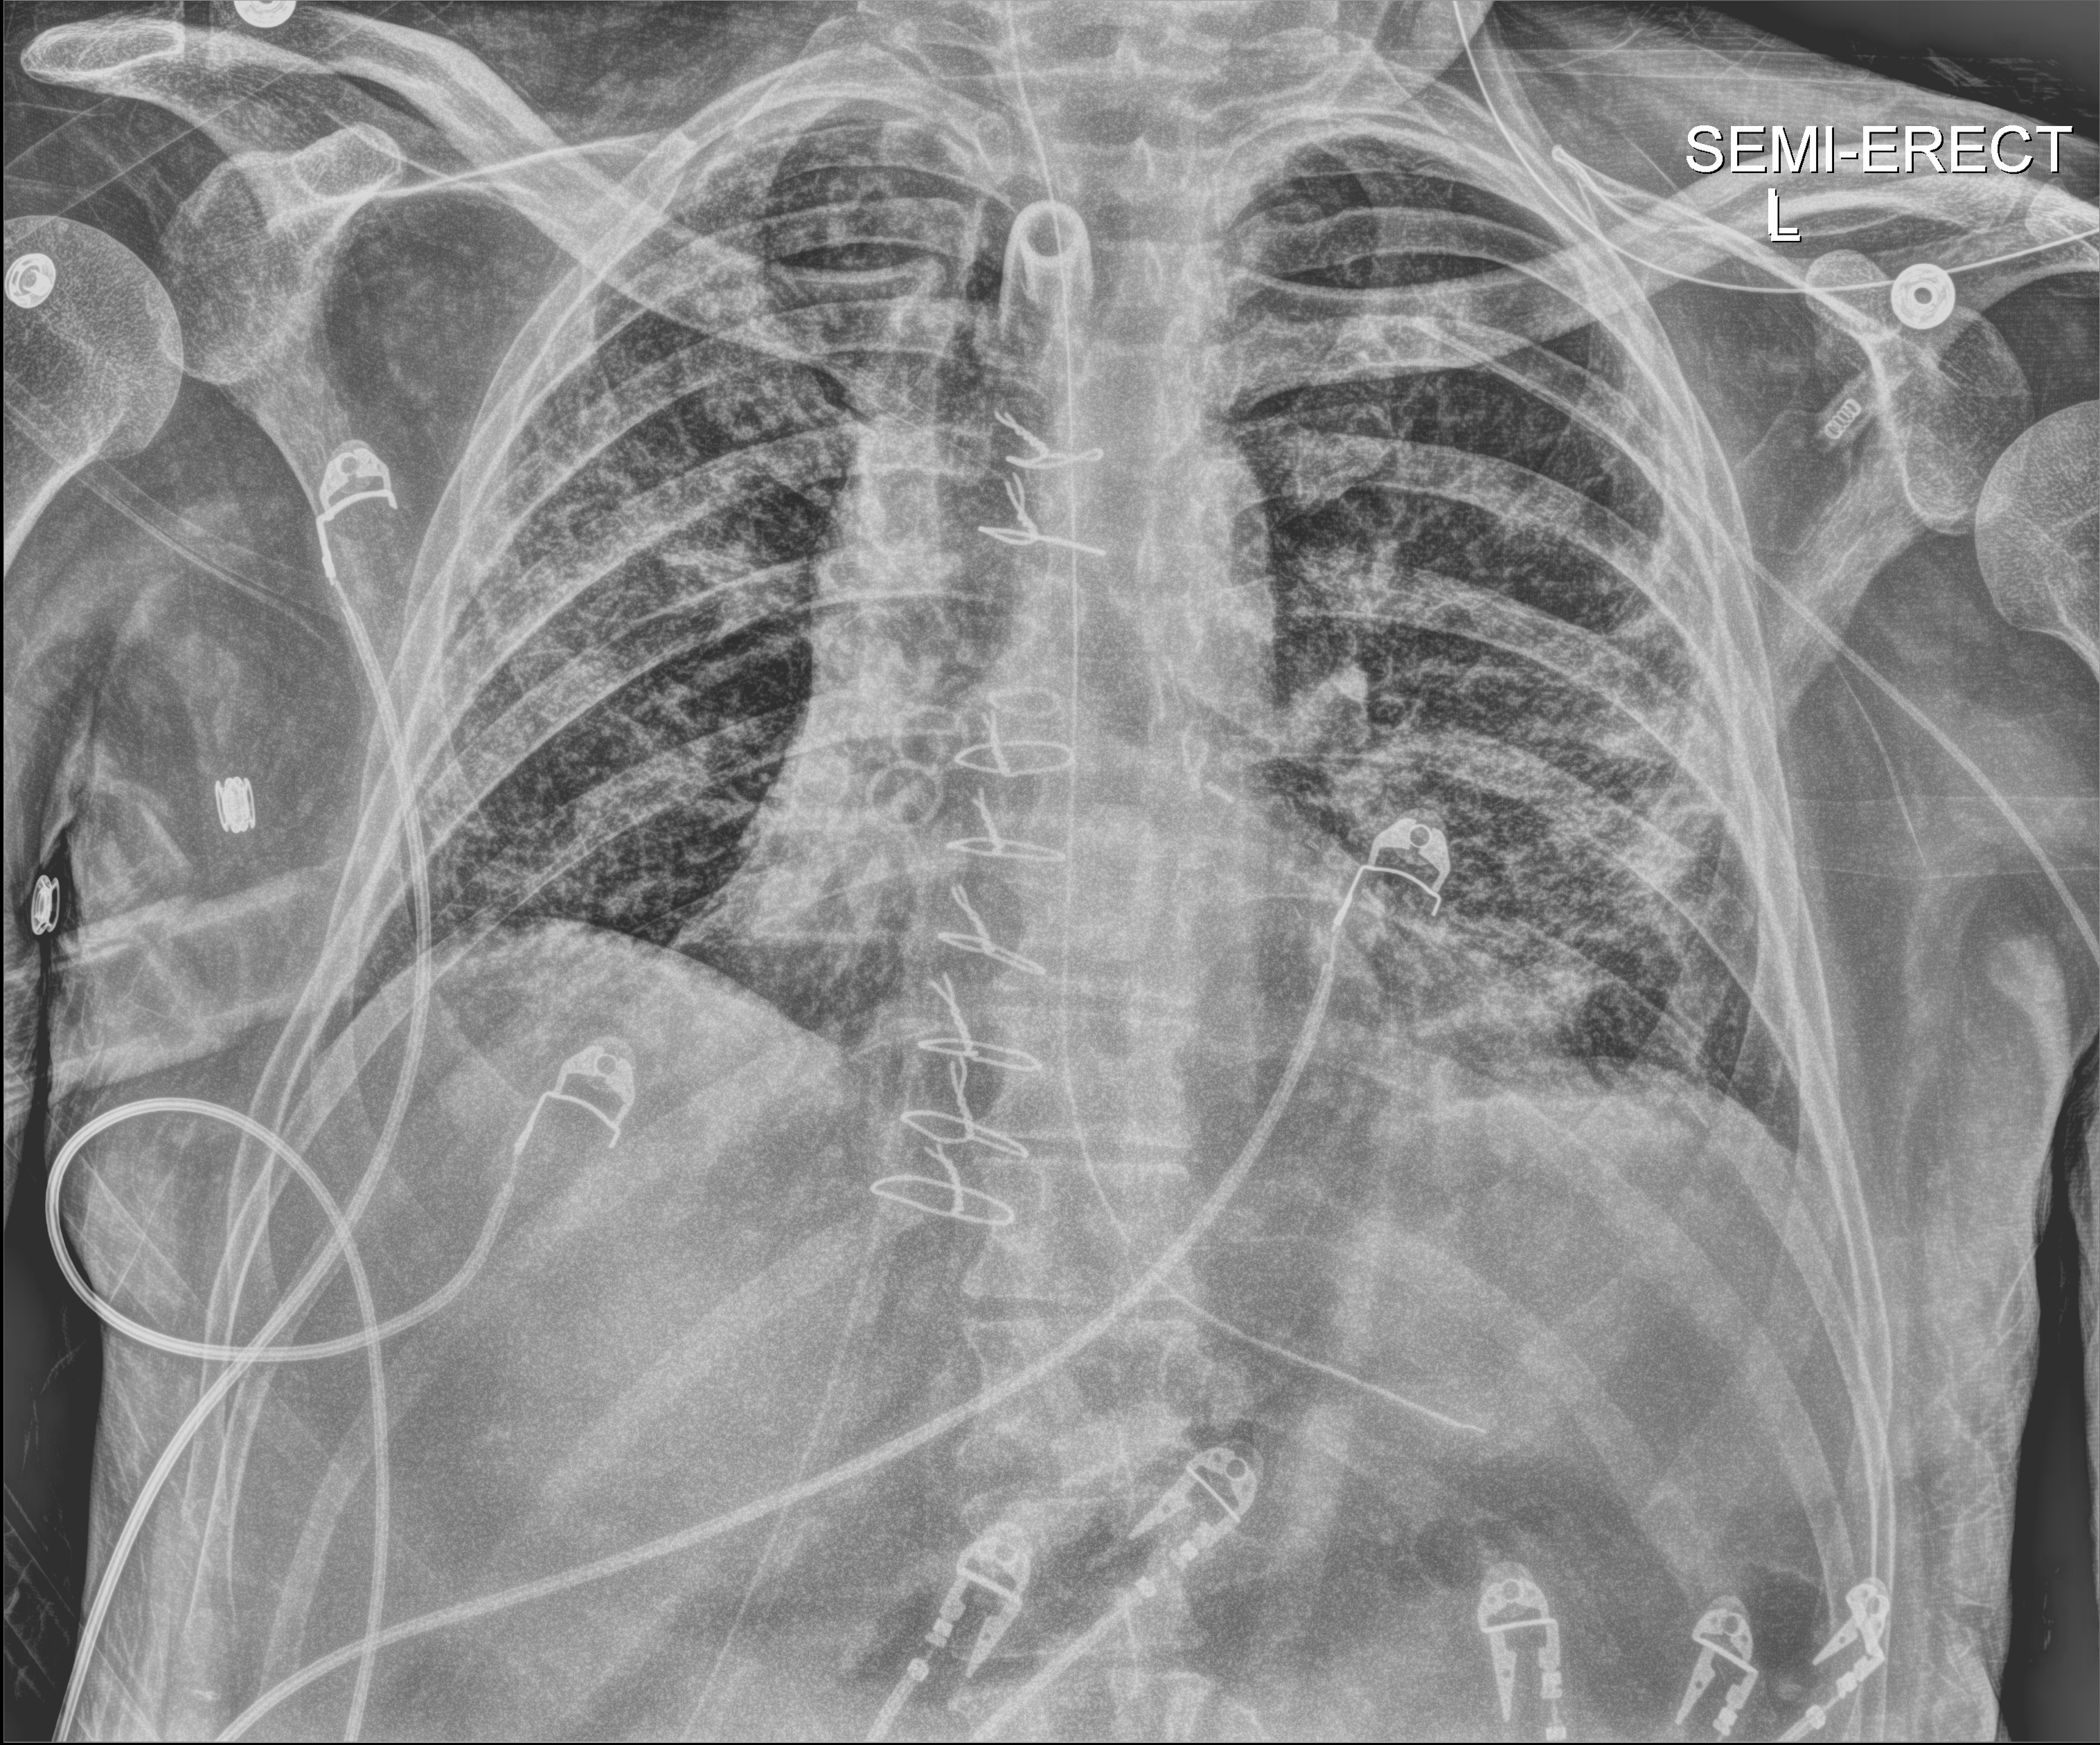
Bedside chest radiograph (digital radiography); anteroposterior (AP) projection. Male patient hospitalised with COVID-19, age 18–59 years.
Hospital-stay facts (about this admission, not read from this image; timing relative to this image not recorded):
- admitted to intensive care during this hospital stay: yes
- length of hospital stay: 63 days